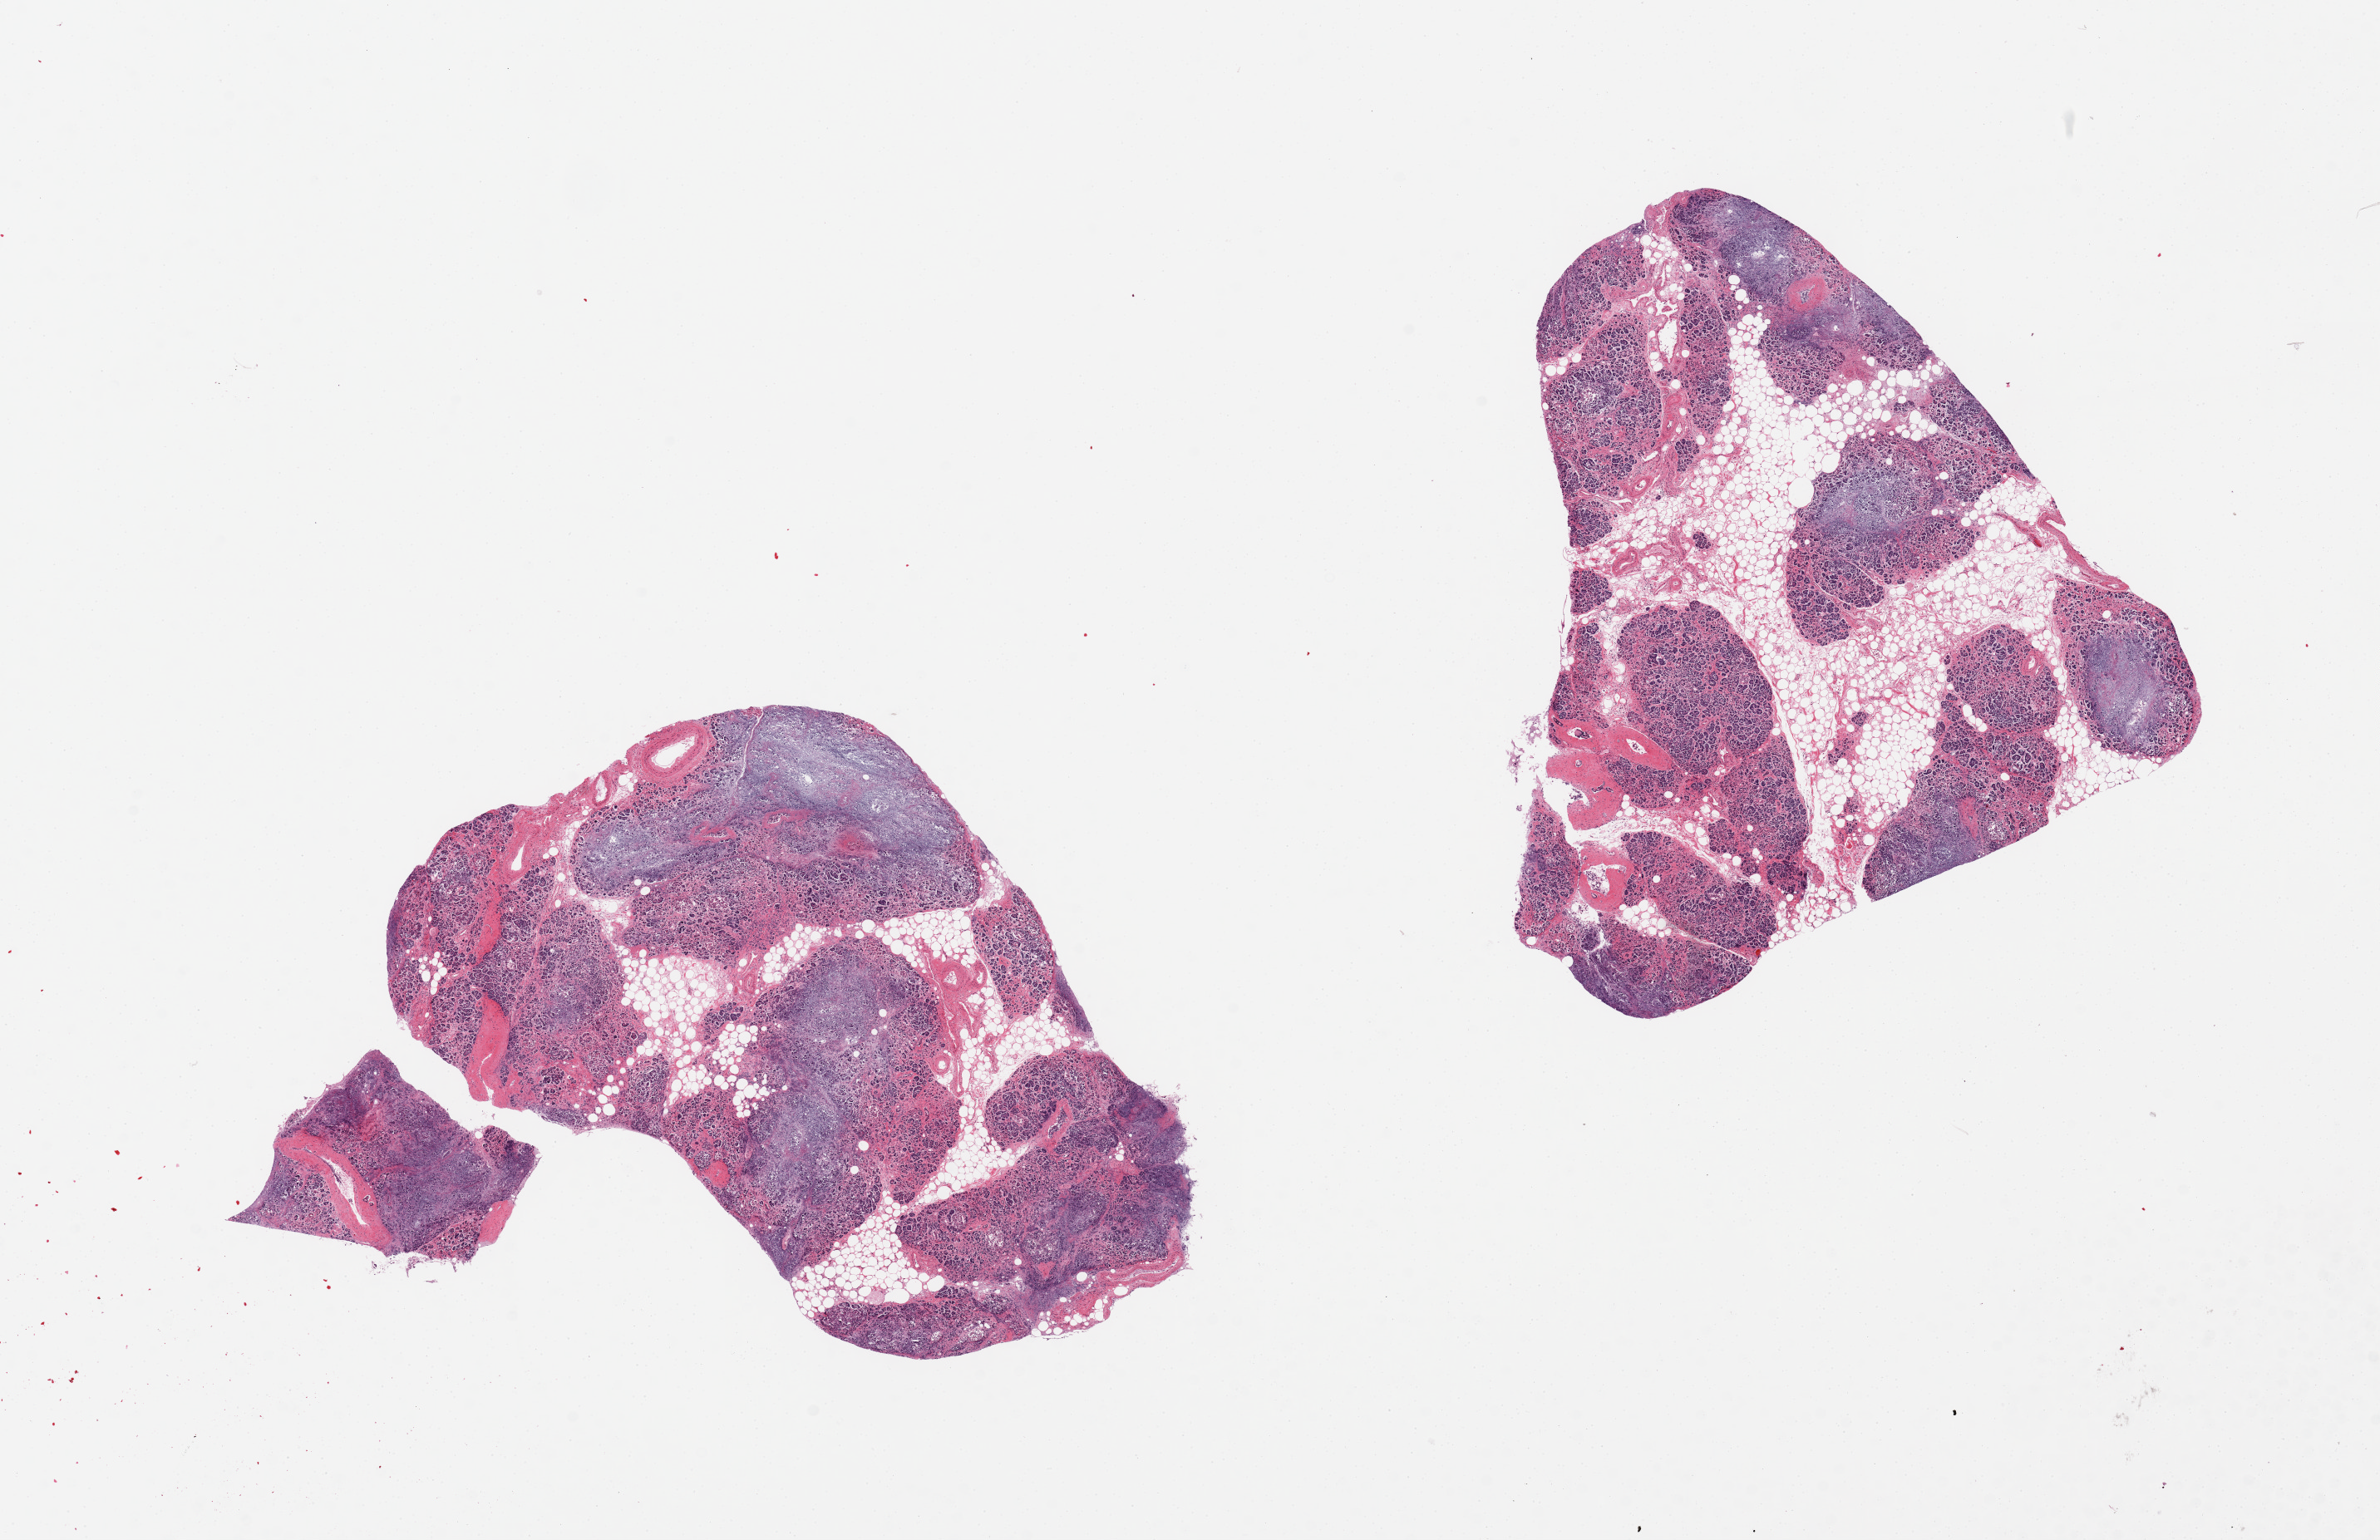
Whole-slide image, haematoxylin and eosin stain, brightfield, low-resolution overview of the scanned area, about 22.6 x 14.7 mm (slide scanned at 20x). PAXgene-fixed paraffin-embedded (PFPE) section. Section of pancreas (target tissue). Donor tissue sample.
Pathologist's review note for this sample: 2 pieces, marked saponification/autolysis, ~30-40% interstitial fat.